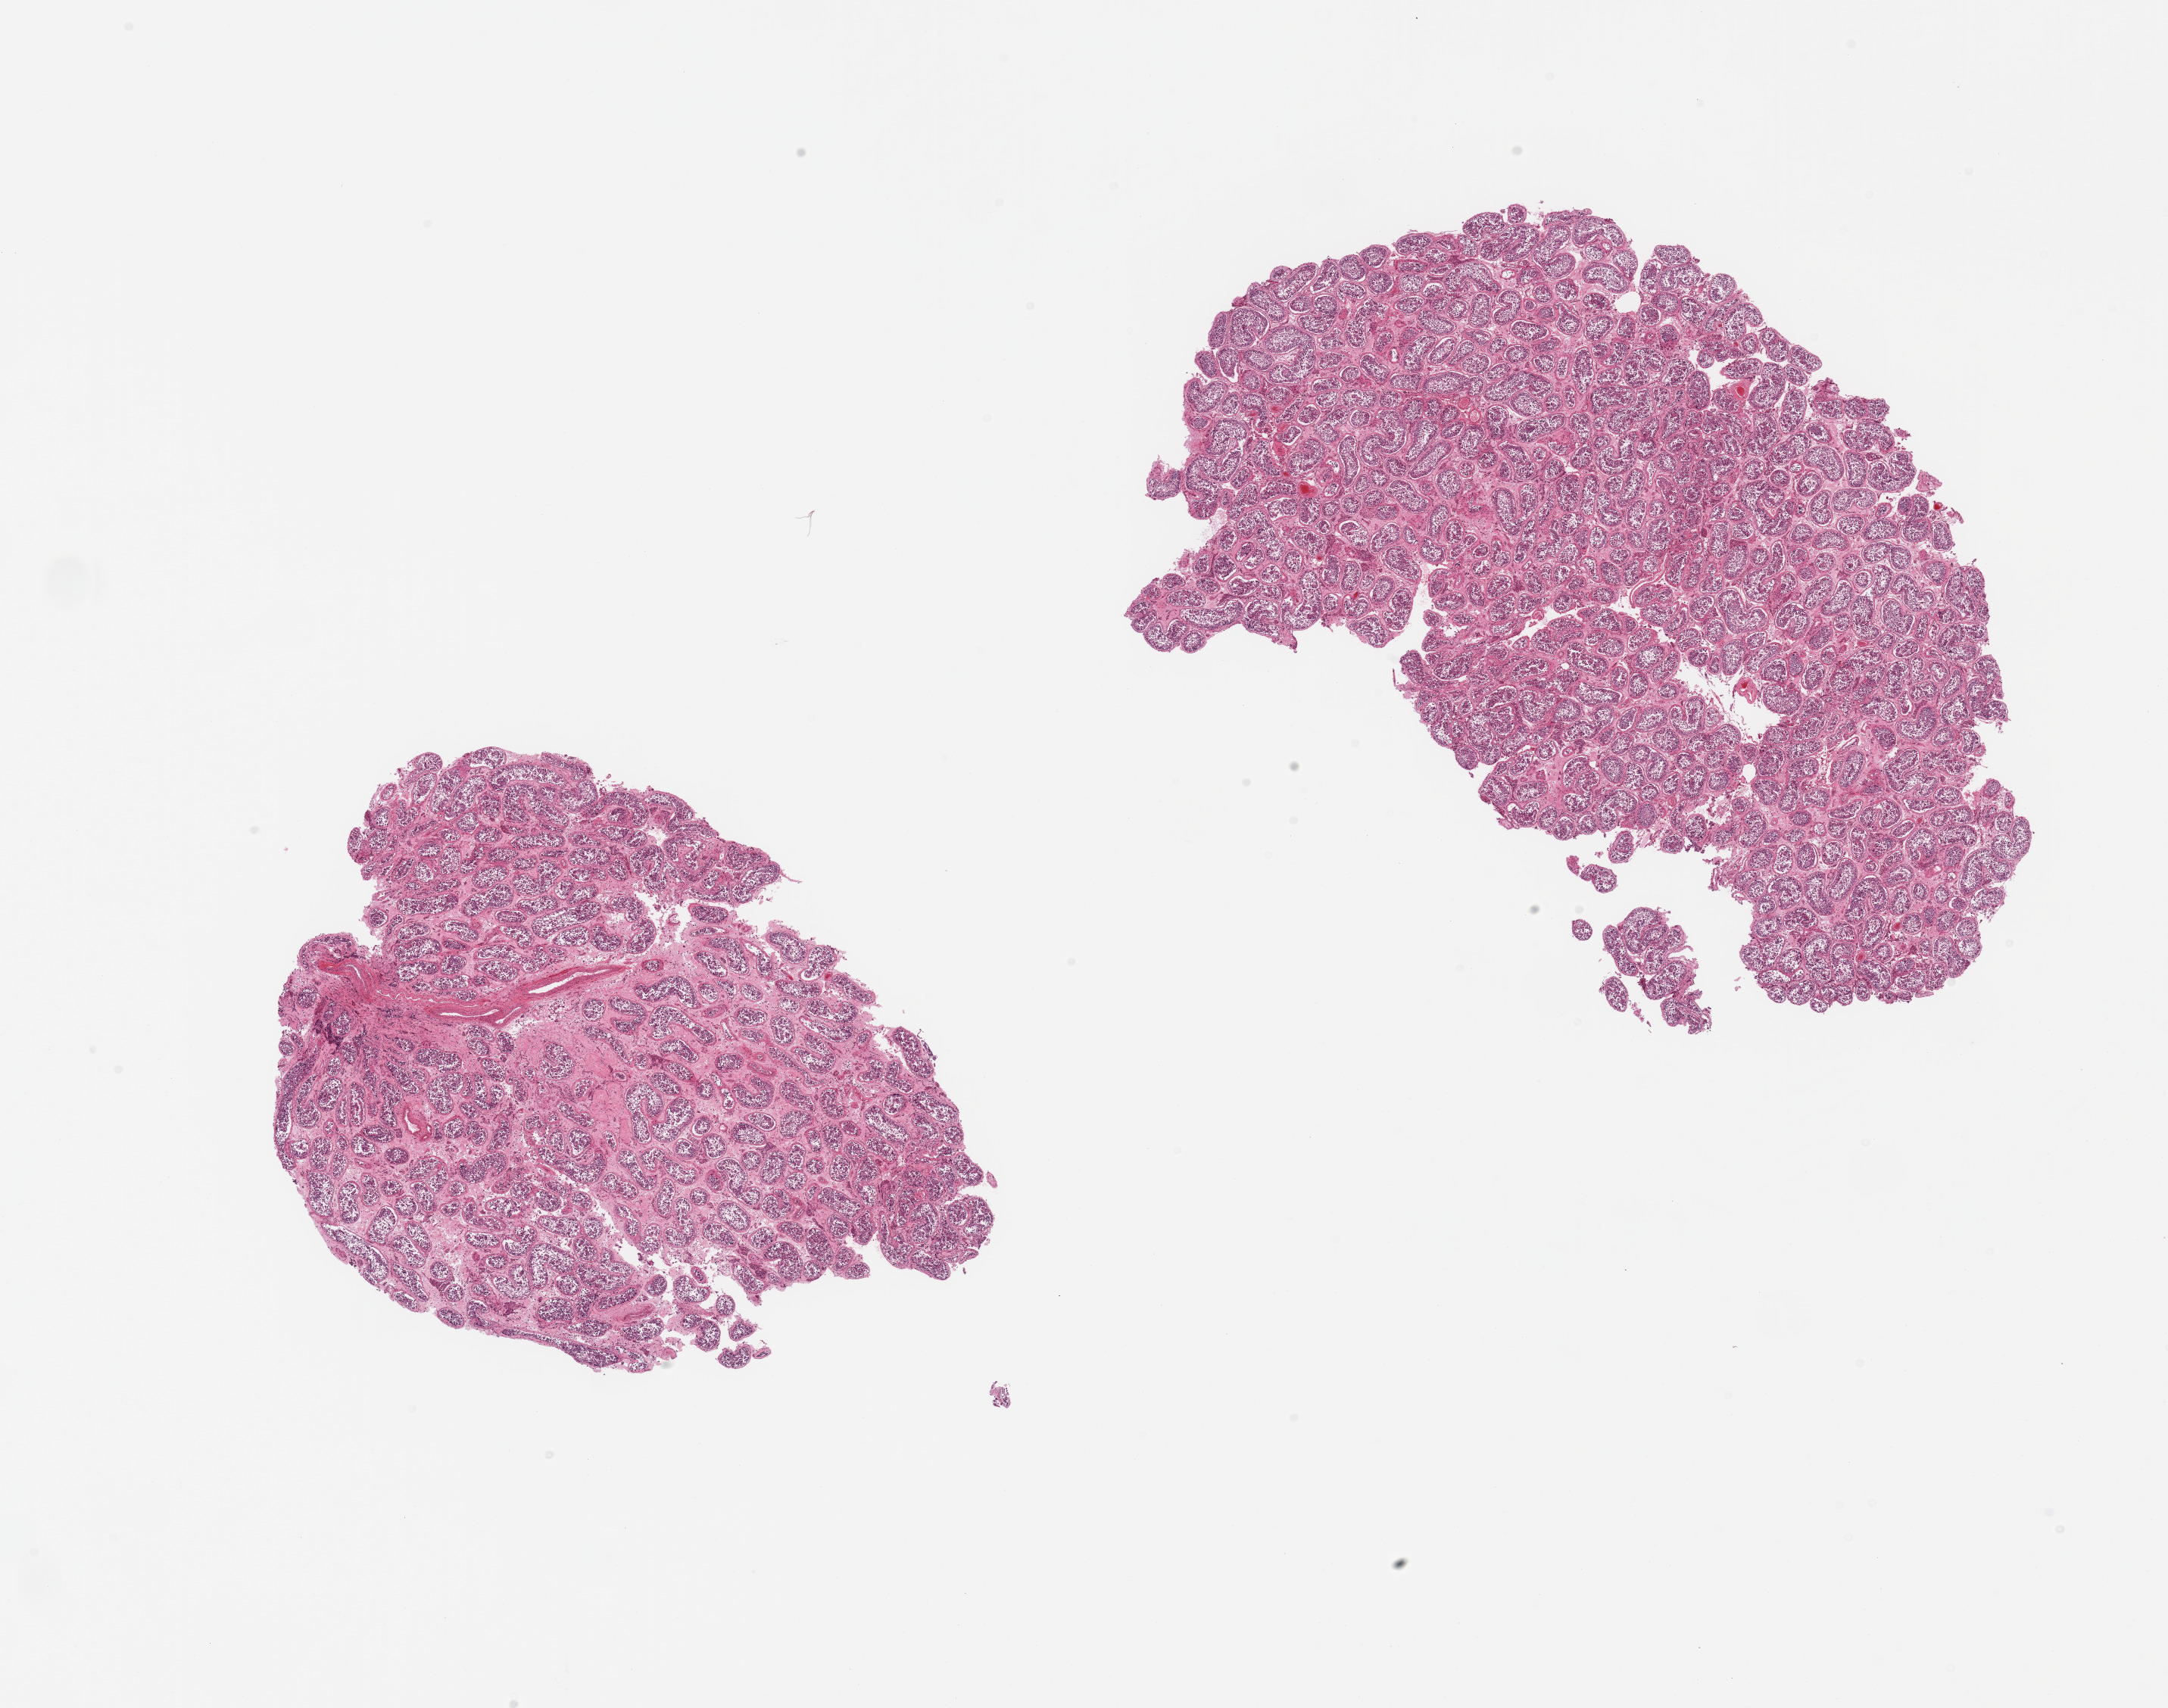
Haematoxylin and eosin whole-slide image, brightfield — a low-resolution overview of the entire scanned area, about 22.6 x 17.8 mm (slide scanned at 20x). PAXgene-fixed, paraffin-embedded tissue. Section of testis (target tissue). Tissue donor sample. Male donor.
- reviewer comment on this tissue sample: 2 pieces; spermatogenesis appears reduced